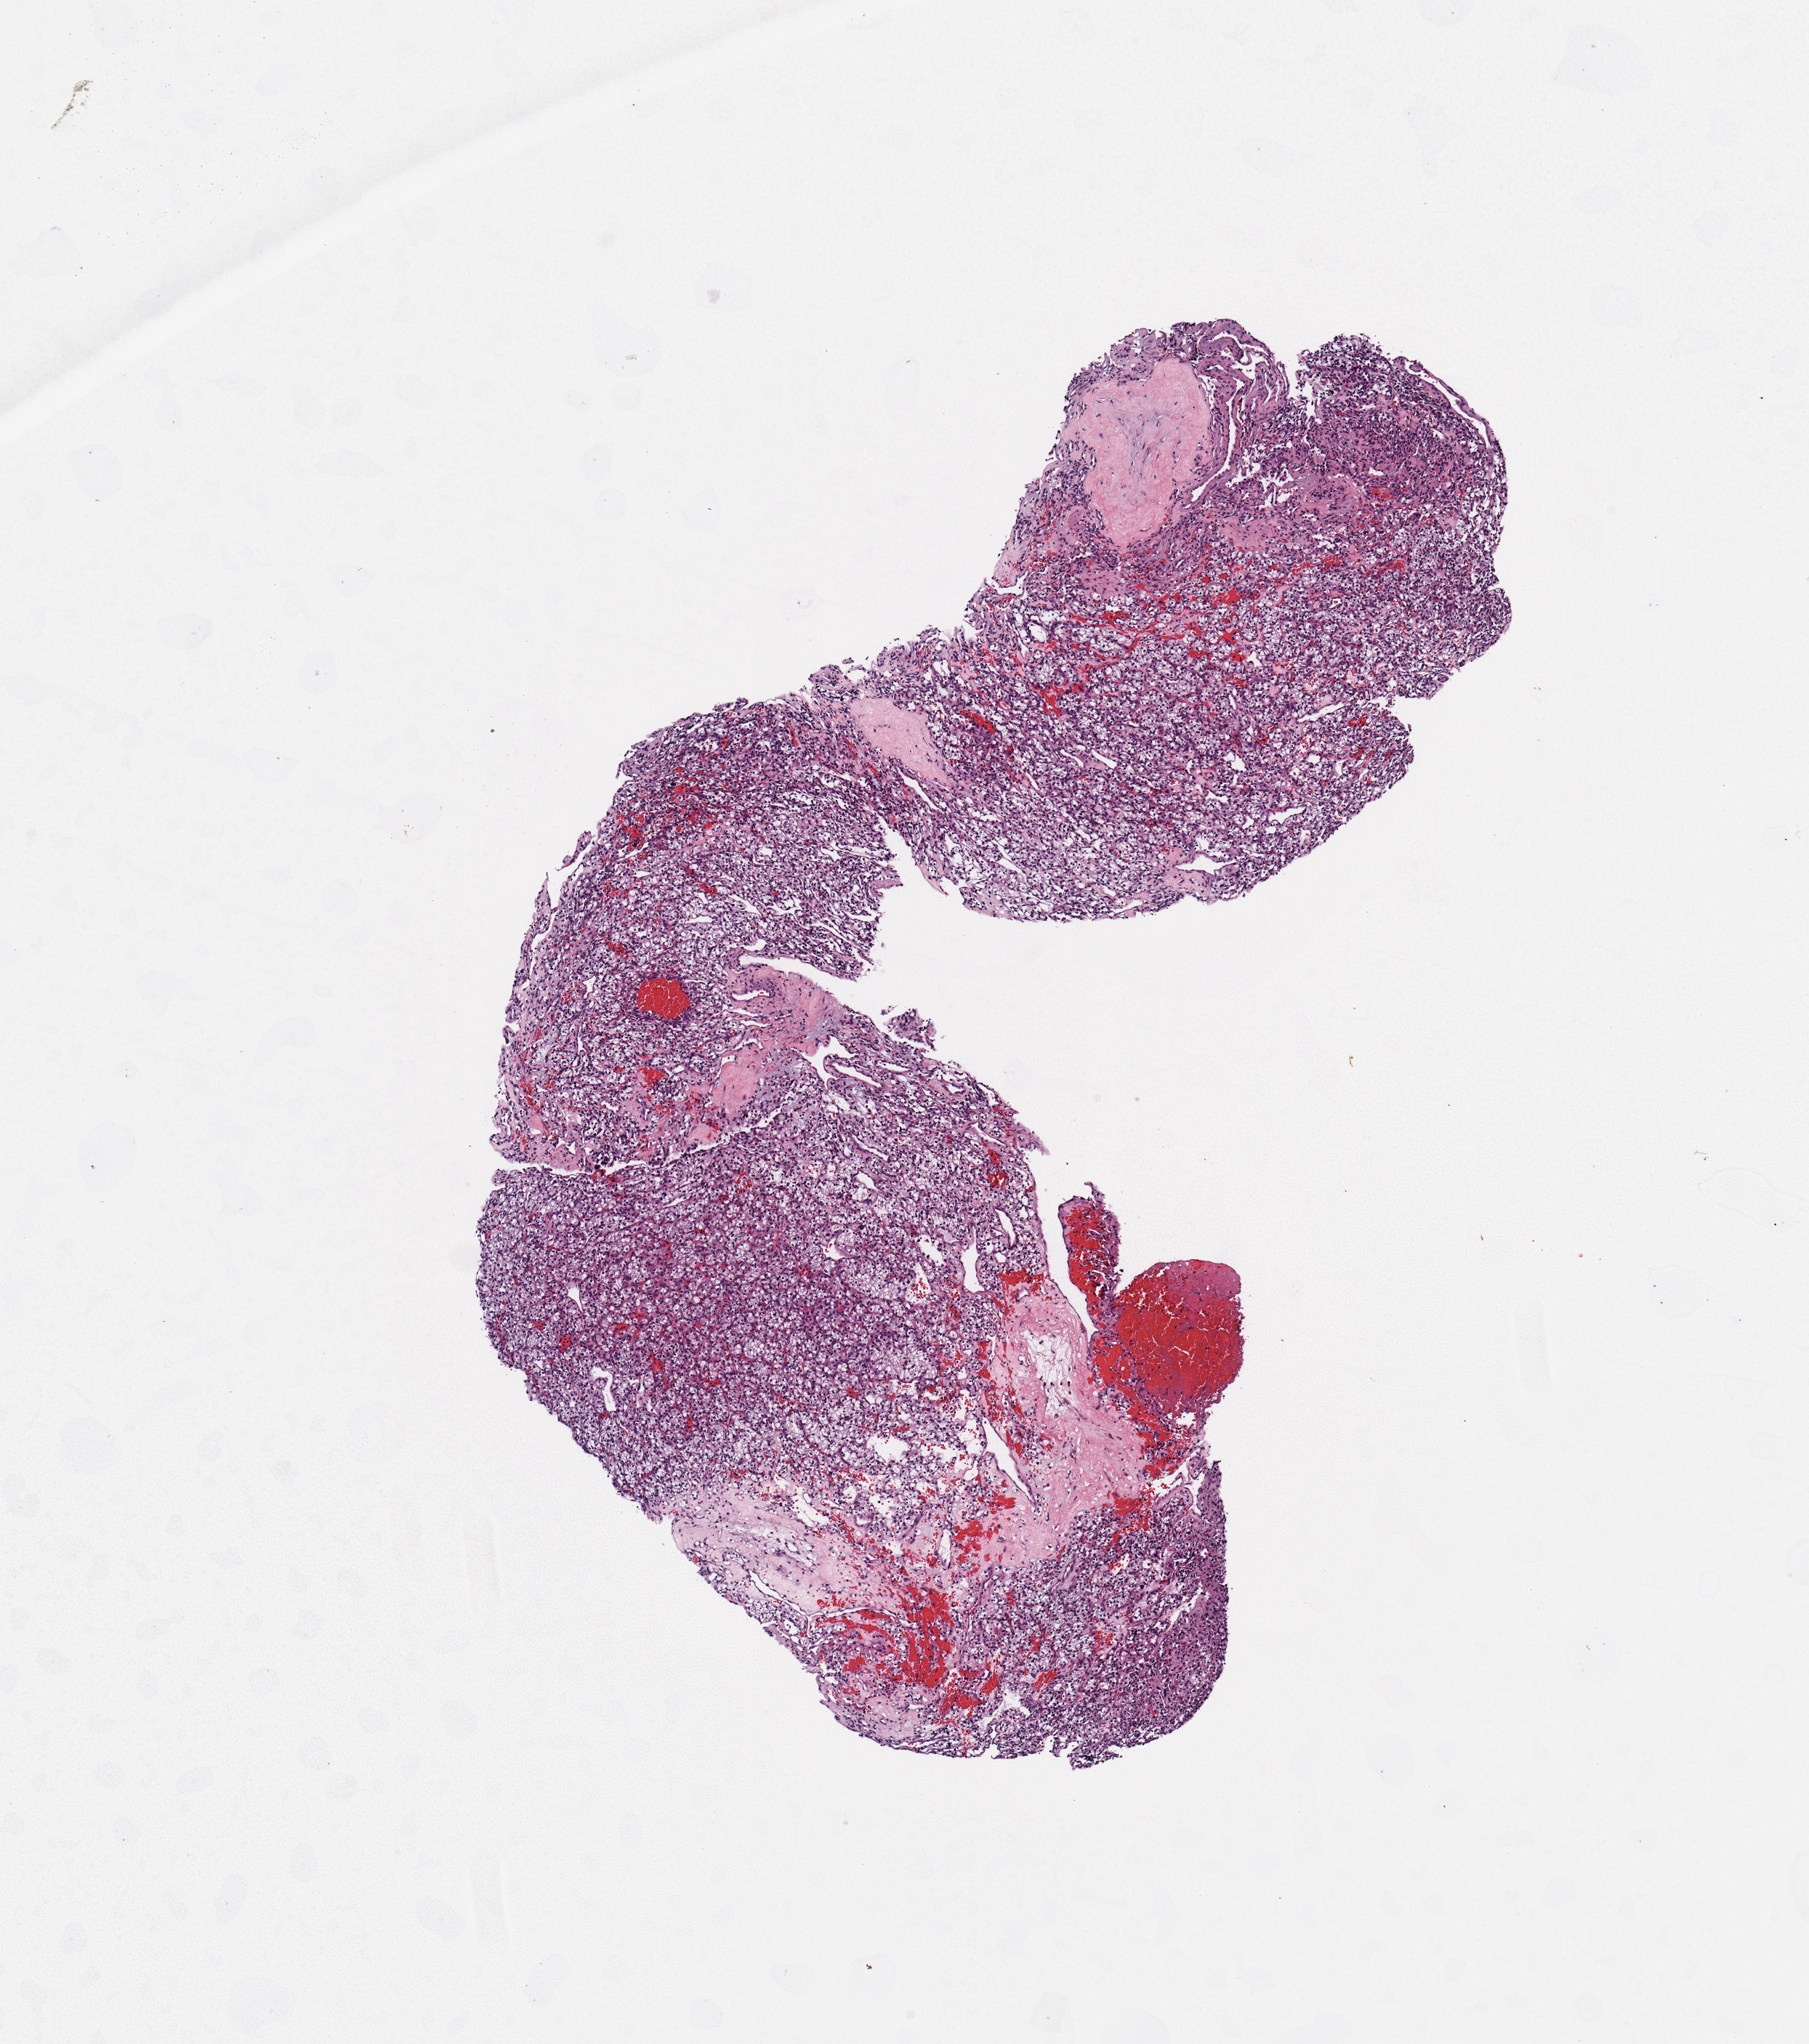
H&E whole-slide image, low-resolution overview of the scanned area, about 4.9 x 5.6 mm (acquisition: 20x scan); tumour tissue sample, sampled site: kidney. Patient: female, age 33 years. Histologic grade: G2 (moderately differentiated). Composition of this section per pathologist review: tumour nuclei 85%, necrosis 5%.
Primary tumour site (as recorded): middle. AJCC pathologic stage: III. Diagnosis: Renal cell carcinoma, NOS.